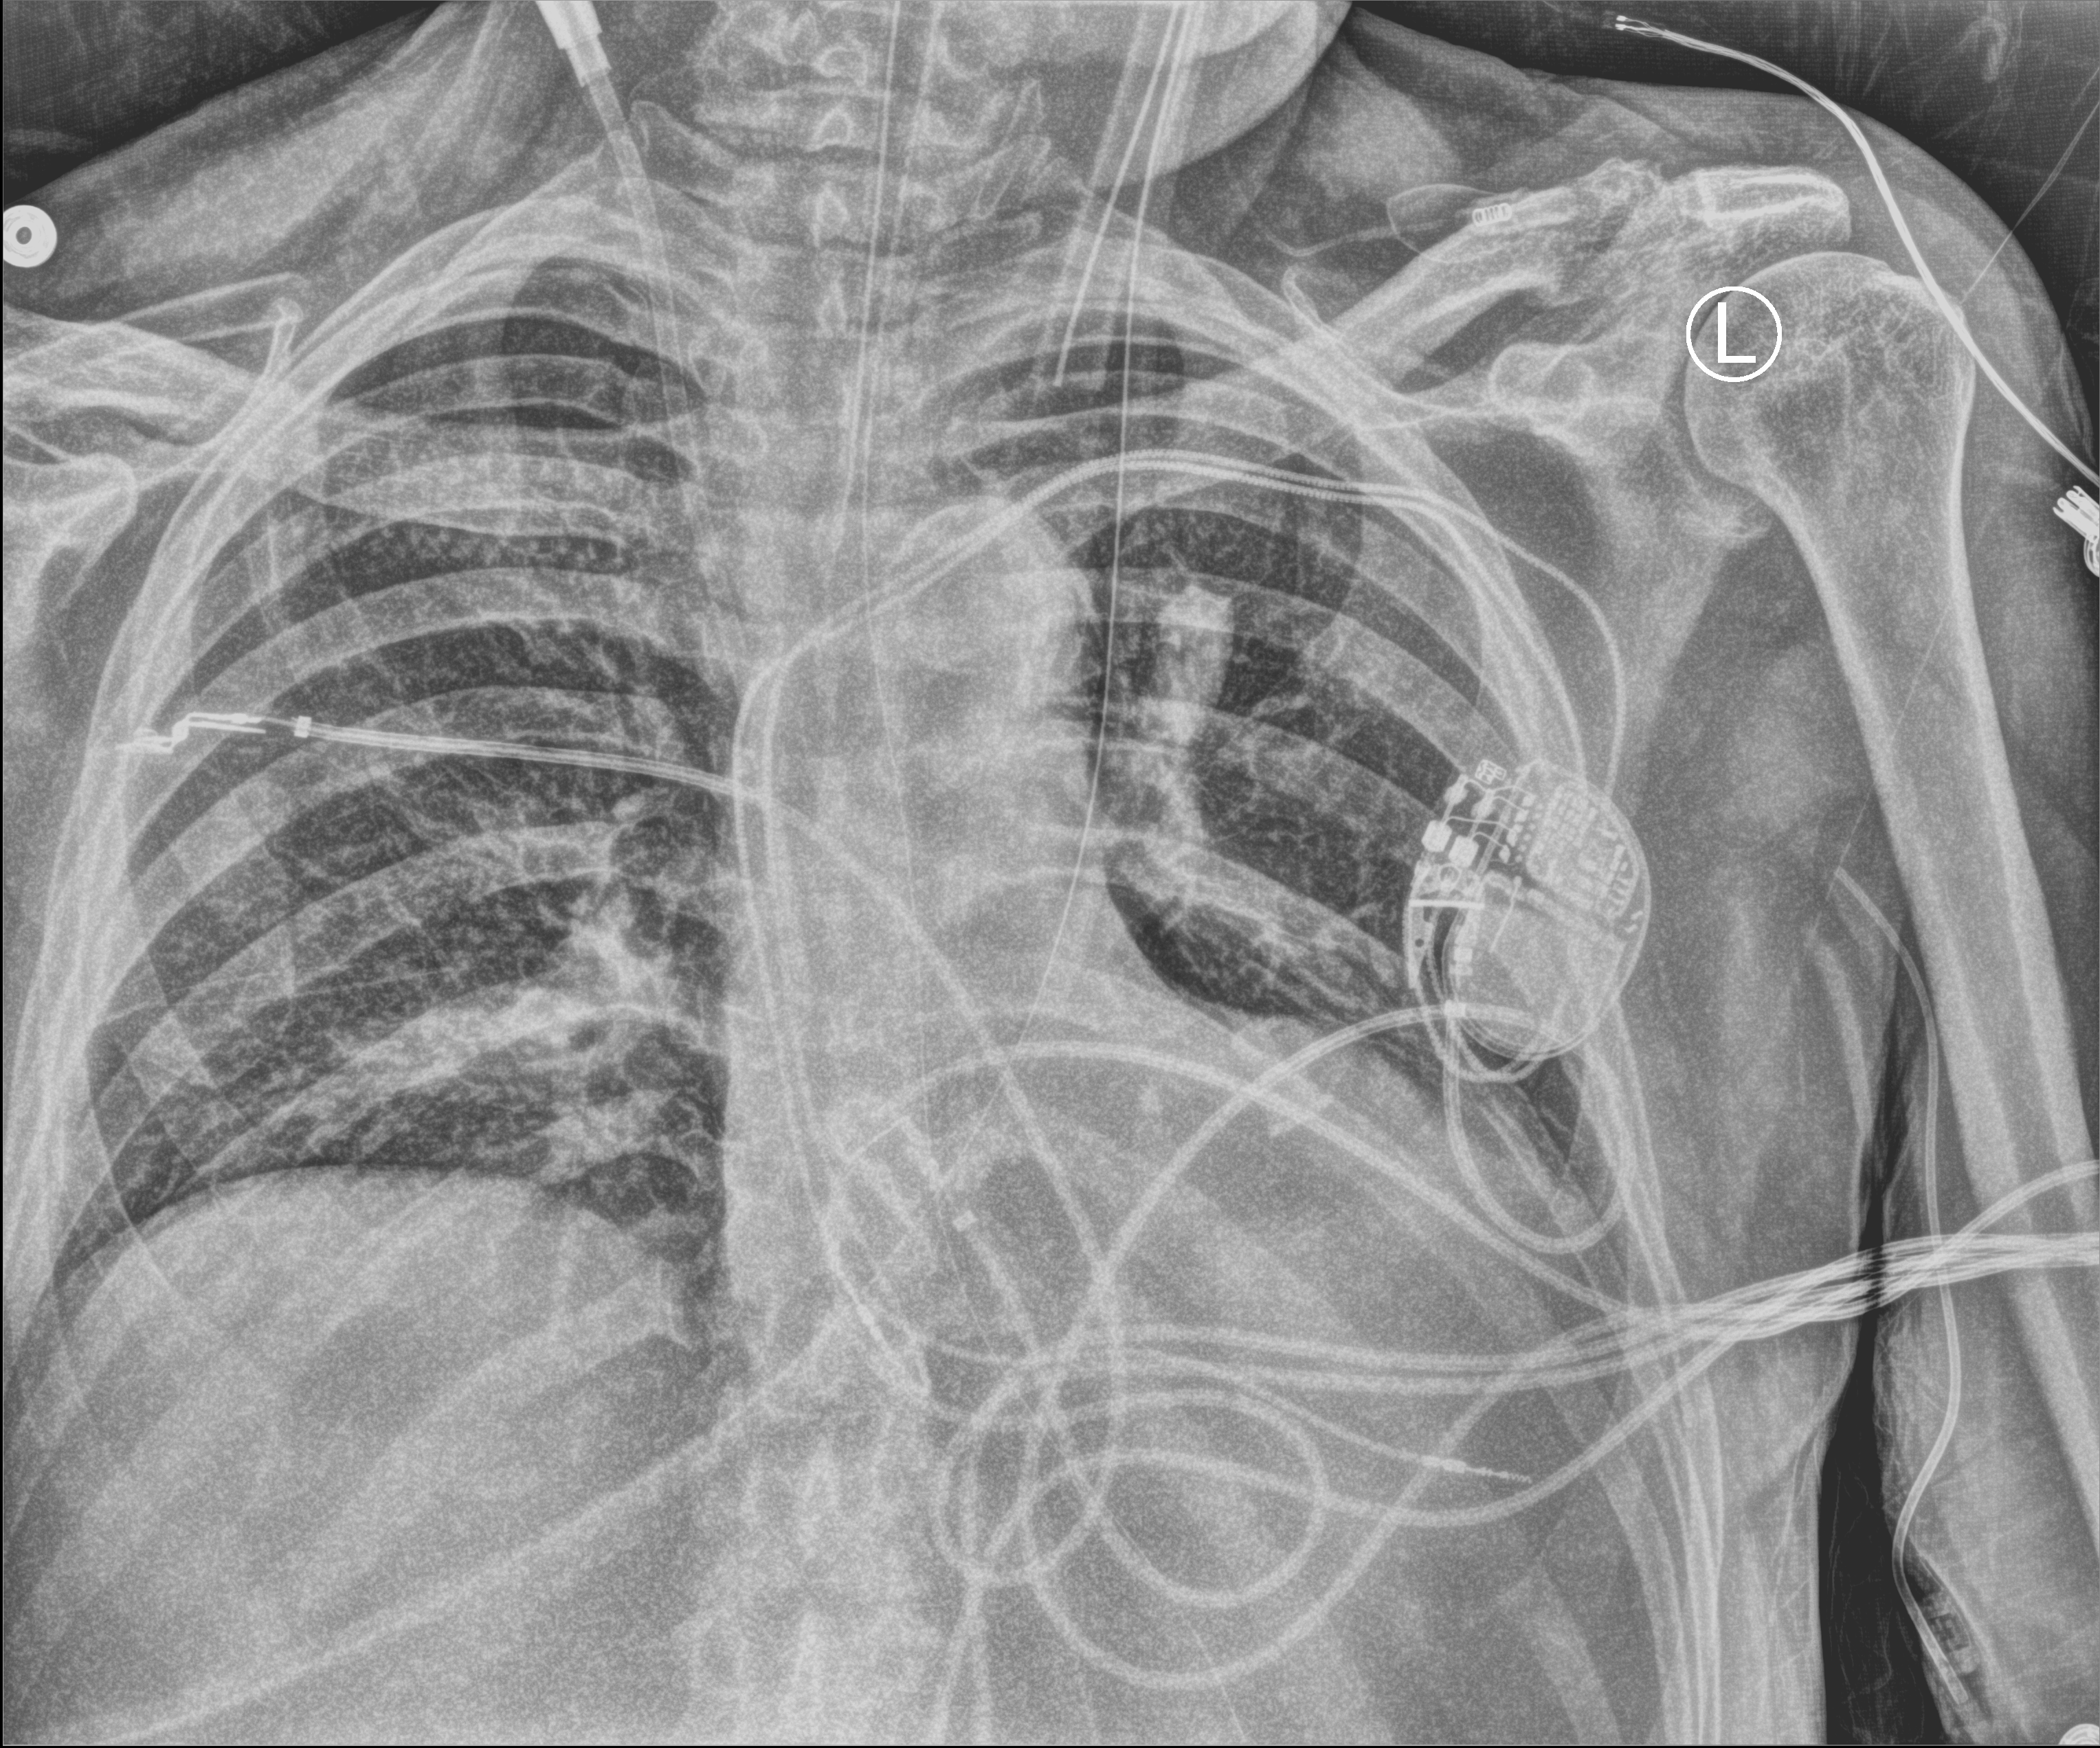
Chest X-ray (portable), anteroposterior (AP) projection. Patient hospitalised with COVID-19; male, aged 60–74 years.
Hospital-stay facts (about this admission, not read from this image; timing relative to this image not recorded): length of hospital stay: 41 days; mechanically ventilated during this hospital stay: yes.